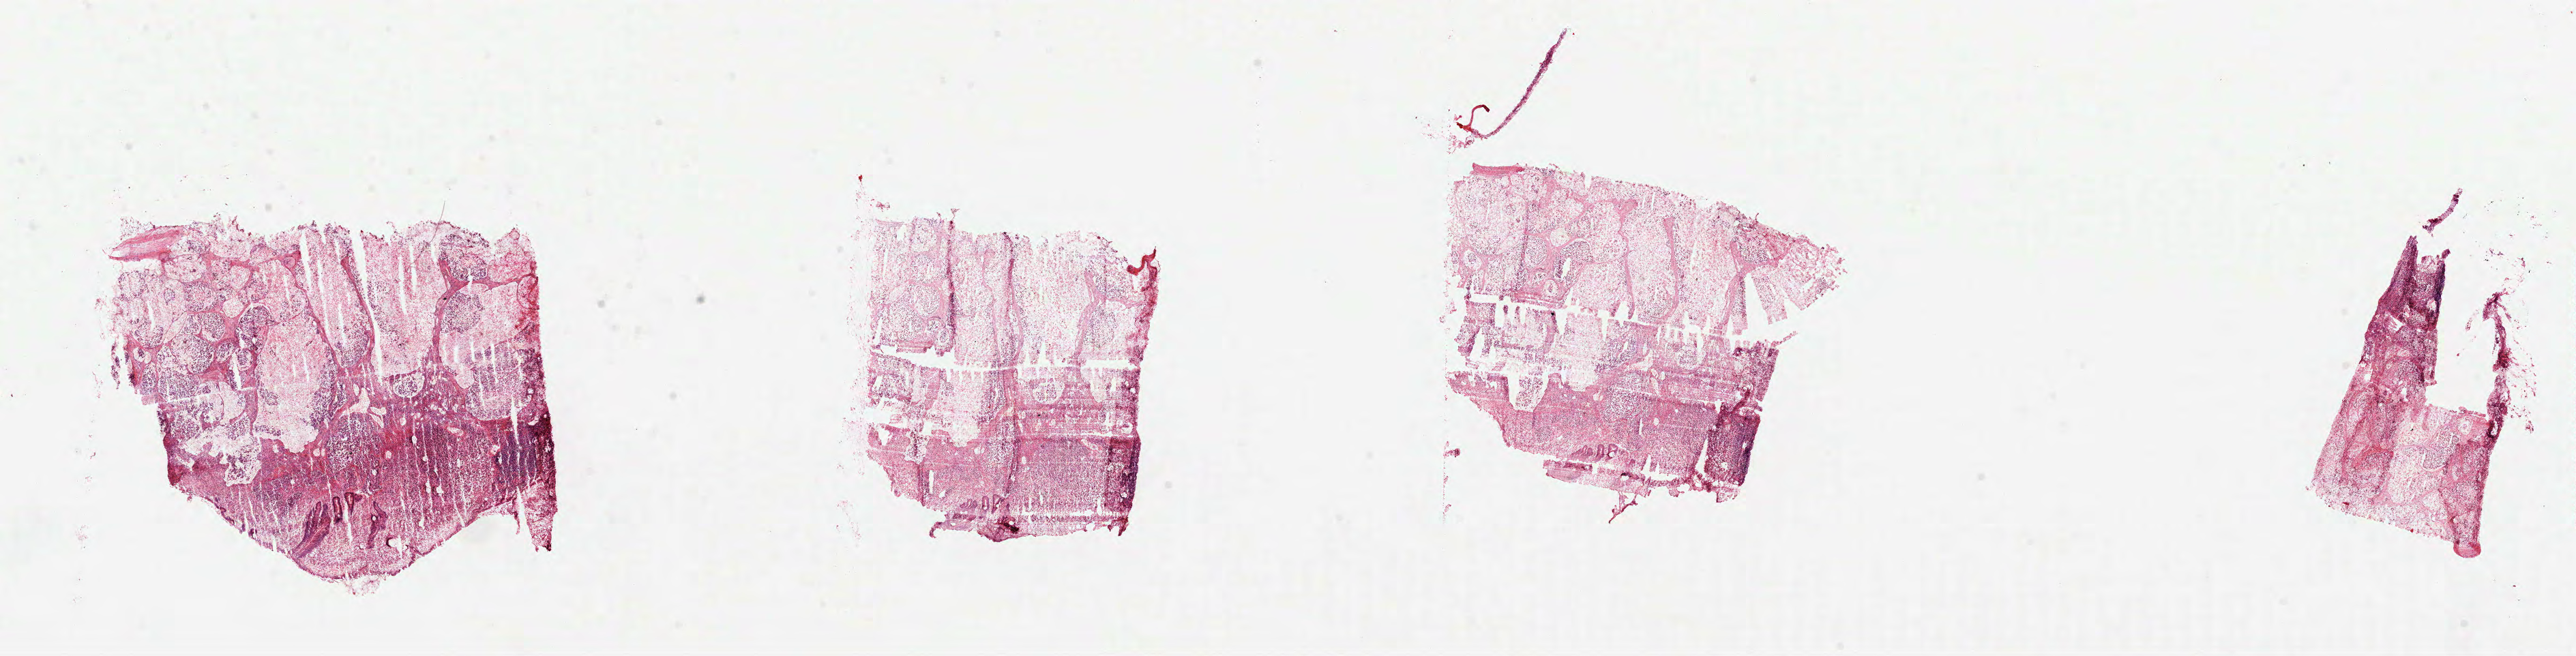
H&E-stained whole-slide image, whole scanned area (about 30.5 x 7.8 mm, acquisition: 40x scan) shown as a low-resolution overview; formalin-fixed paraffin-embedded (FFPE) diagnostic section; primary tumour sample from the rectum. Patient: female, age at initial diagnosis 37 years.
Lymph nodes positive (case pathology): 30 of 30 examined. Diagnosis: Mucinous adenocarcinoma (rectosigmoid junction).